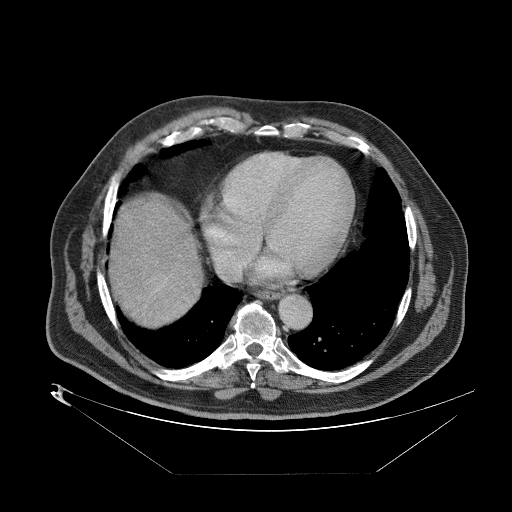
Contrast-enhanced abdominal CT (liver protocol), one axial slice. One of 2 acquisitions stored at this slice position. Soft-tissue window (W 400 / L 40 HU). 2.5 mm slice thickness. 512 × 512 image matrix. Case-level facts recorded for this patient, not image findings: diagnosis: hepatocellular carcinoma (patient treated with transarterial chemoembolisation; whether this scan precedes or follows treatment is not stated here); TNM stage (as recorded): Stage-II; Child-Pugh class: B; tumour differentiation: moderately differentiated; tumour size: 4 cm.
Annotated regions visible in this slice (semi-automatically segmented with operator editing):
- abdominal aorta: bounding box [x1, y1, x2, y2] px = [276, 292, 311, 327]
- liver parenchyma outside the tumour (the mass and vessels are separate outlines, so this box may not span the whole liver): [110, 194, 196, 316]